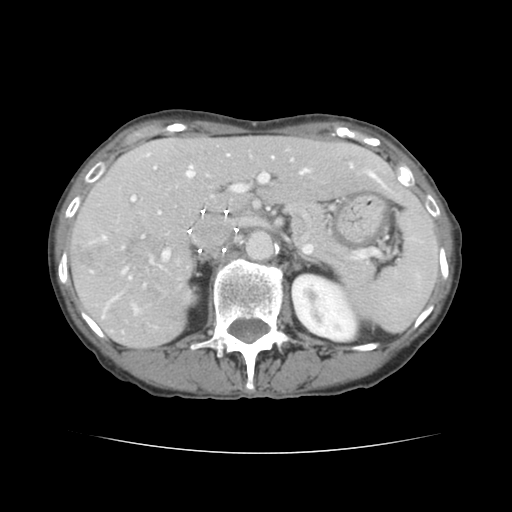
Contrast-enhanced abdominal CT, one axial slice; position 86 of 136 along the scan axis; 120 kVp; intravenous contrast given; soft-tissue window (W 400 / L 40 HU); 512 × 512 image matrix, field of view 319 × 319 mm. Female patient, age 77 years. Case-level facts recorded for this patient, not image findings: diagnosis: colorectal cancer liver metastases, imaged before liver resection; multiple liver metastases: yes; largest metastasis: 3 cm.
Structures marked on this image (manually delineated by an expert):
- hepatic veins: bounding box (x1, y1, x2, y2) in pixels: (187, 155, 382, 183)
- liver: (71, 136, 418, 347)
- planned liver remnant (the part of the liver to remain after resection): (153, 137, 417, 211)
- portal vein (with intrahepatic branches): (103, 159, 293, 311)
- liver metastasis: (74, 247, 94, 266)